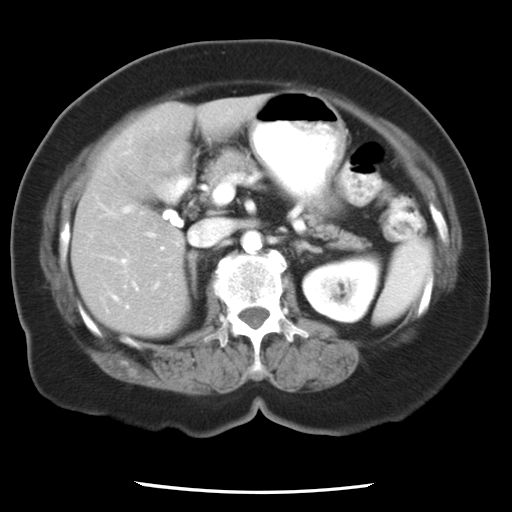
Contrast-enhanced abdominal CT, one axial slice; position 11 of 24 along the scan axis; reconstruction kernel STANDARD; 120 kVp; intravenous contrast given; soft-tissue window (W 400 / L 40 HU); 7.5 mm slice thickness; 512 × 512 image matrix, field of view 312 × 312 mm. Female patient, age 71 years. From the clinical record (not read from this slice): diagnosis: colorectal cancer liver metastases, imaged before liver resection; multiple liver metastases: no; largest metastasis: 4.3 cm.
Outlined on this slice (manually delineated by an expert):
- hepatic veins: box from (x=114, y=206) to (x=137, y=307) px
- liver: (x=73, y=94)–(x=275, y=336)
- planned liver remnant (the part of the liver to remain after resection): (x=73, y=106)–(x=188, y=336)
- portal vein (with intrahepatic branches): (x=110, y=228)–(x=171, y=290)